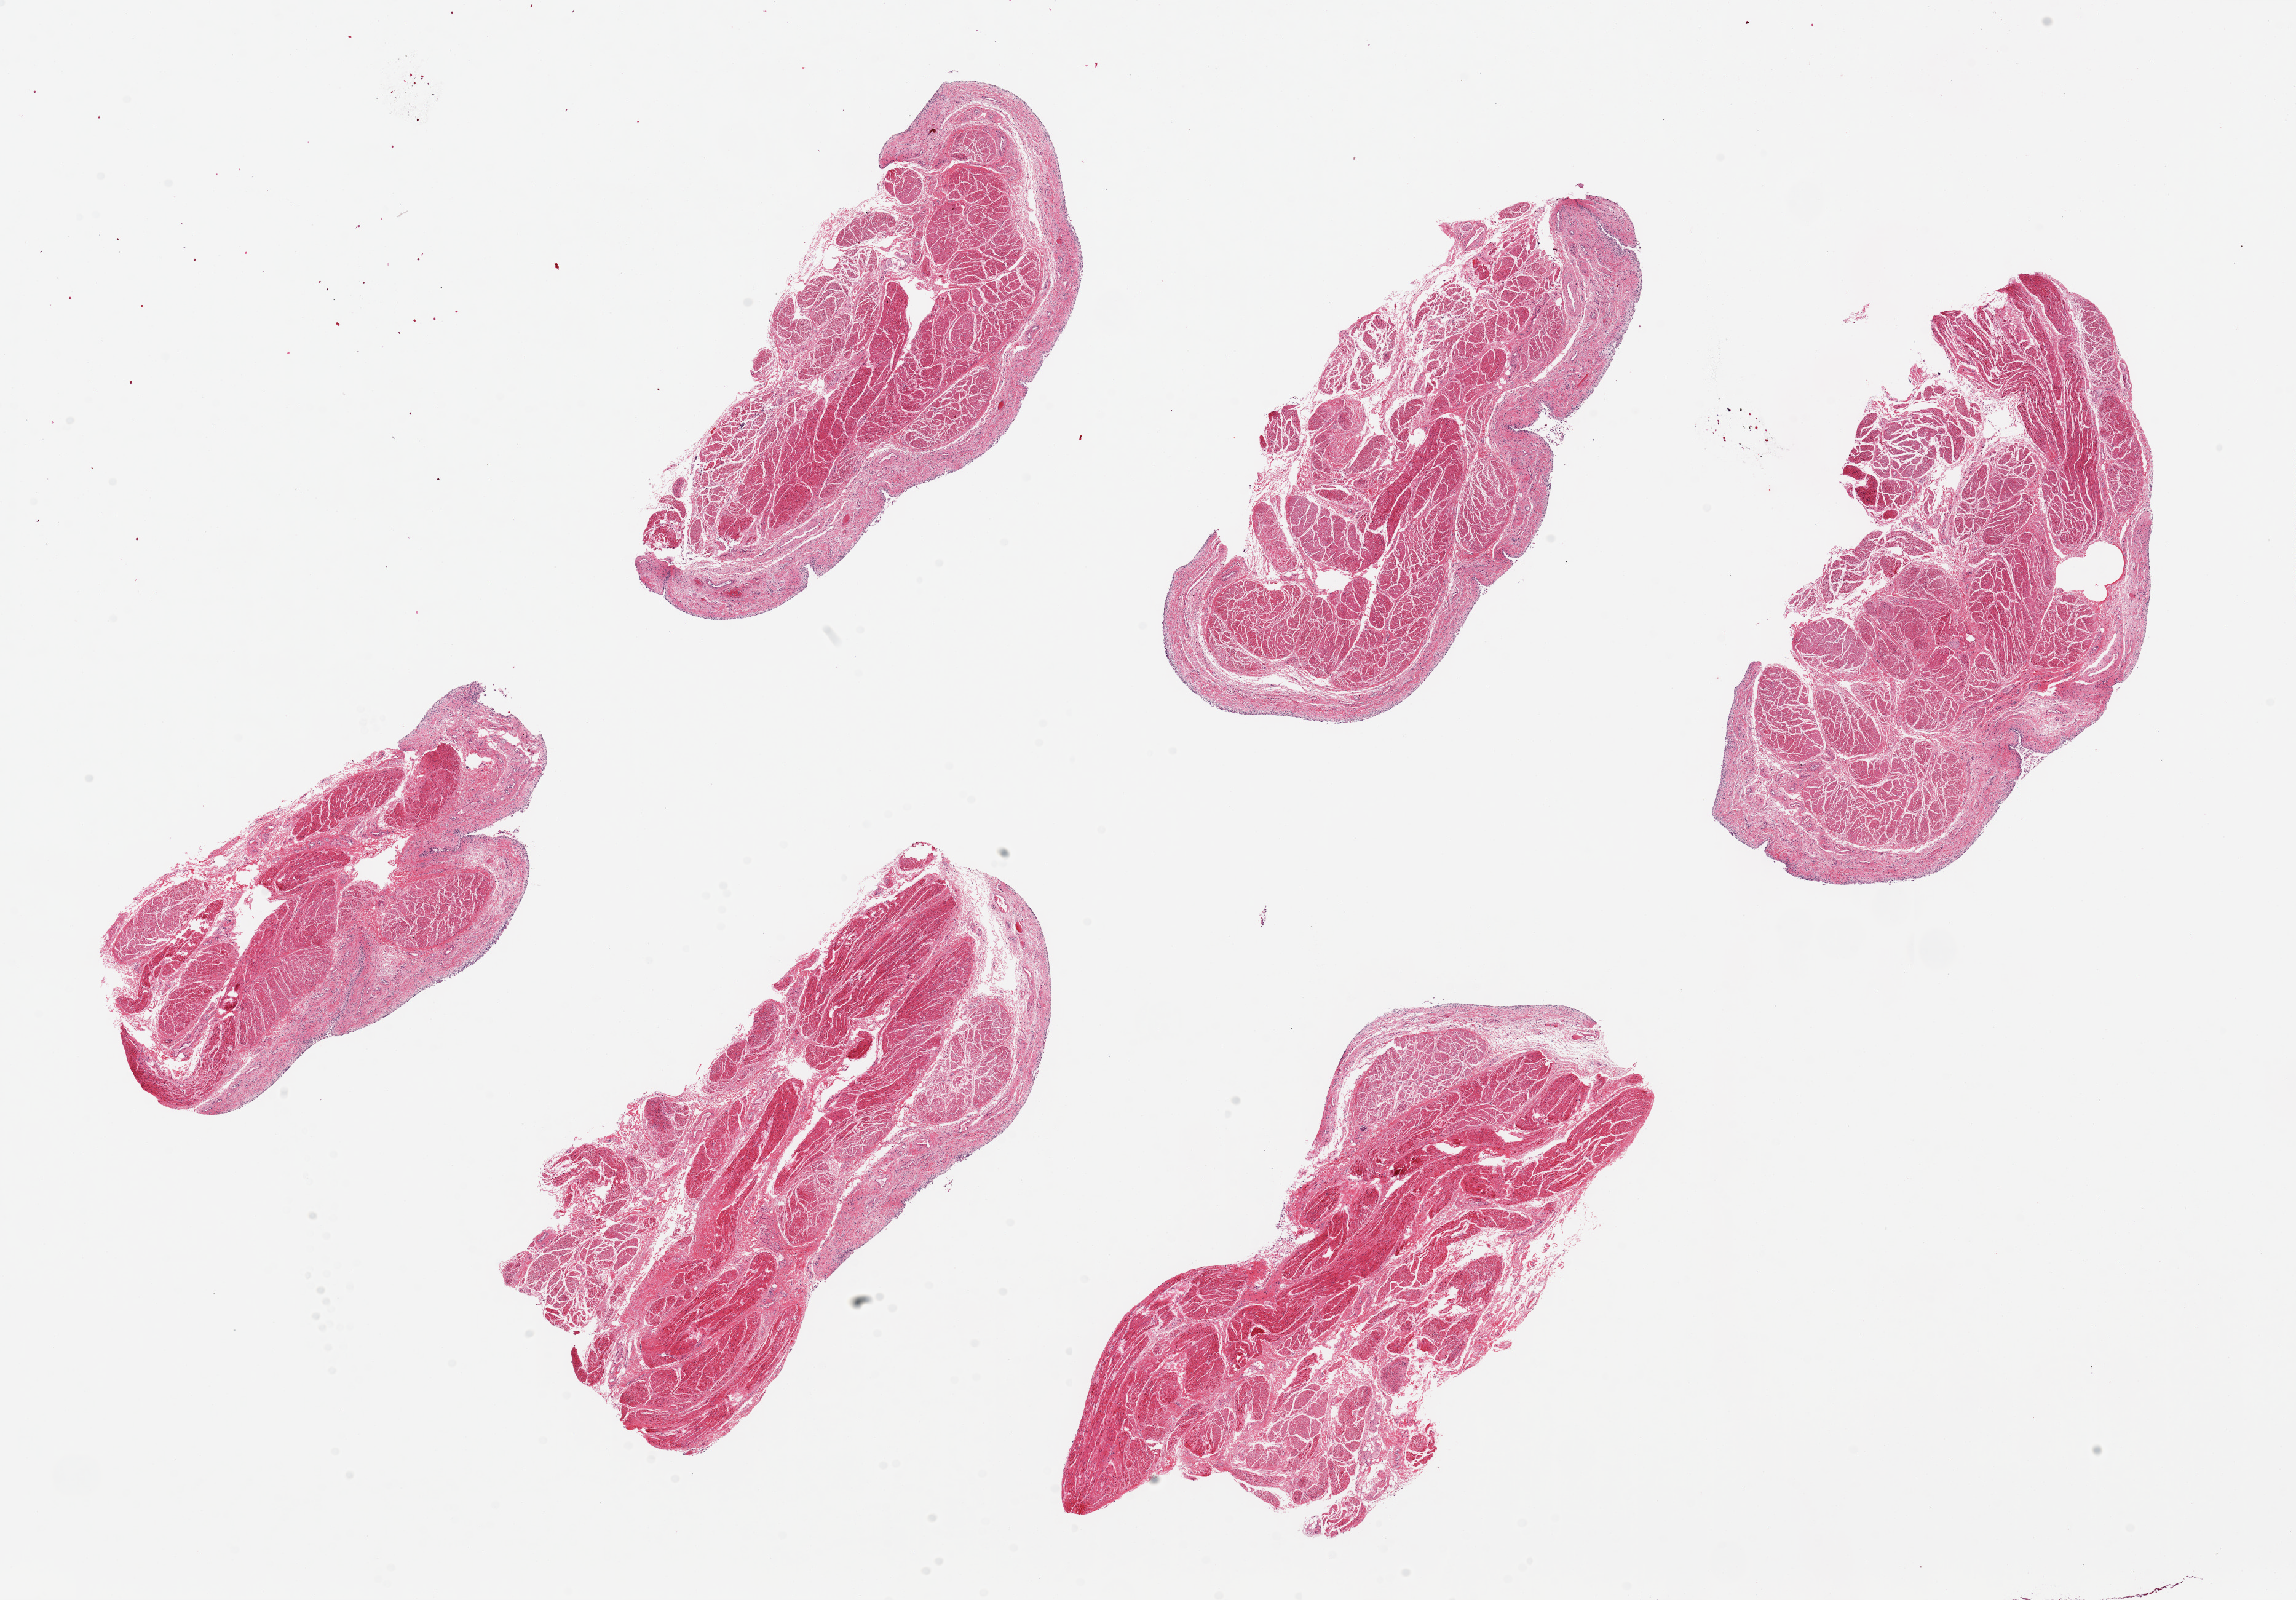
H&E whole-slide image — low-resolution overview of the scanned area, about 29.5 x 20.6 mm (acquisition: 20x scan), PAXgene-fixed paraffin-embedded (PFPE) section, target tissue: vagina, tissue donor sample. Donor: female.
Reviewer comment on this tissue sample: 6 pieces ~8x3mm. Mucosa completely sloughed.